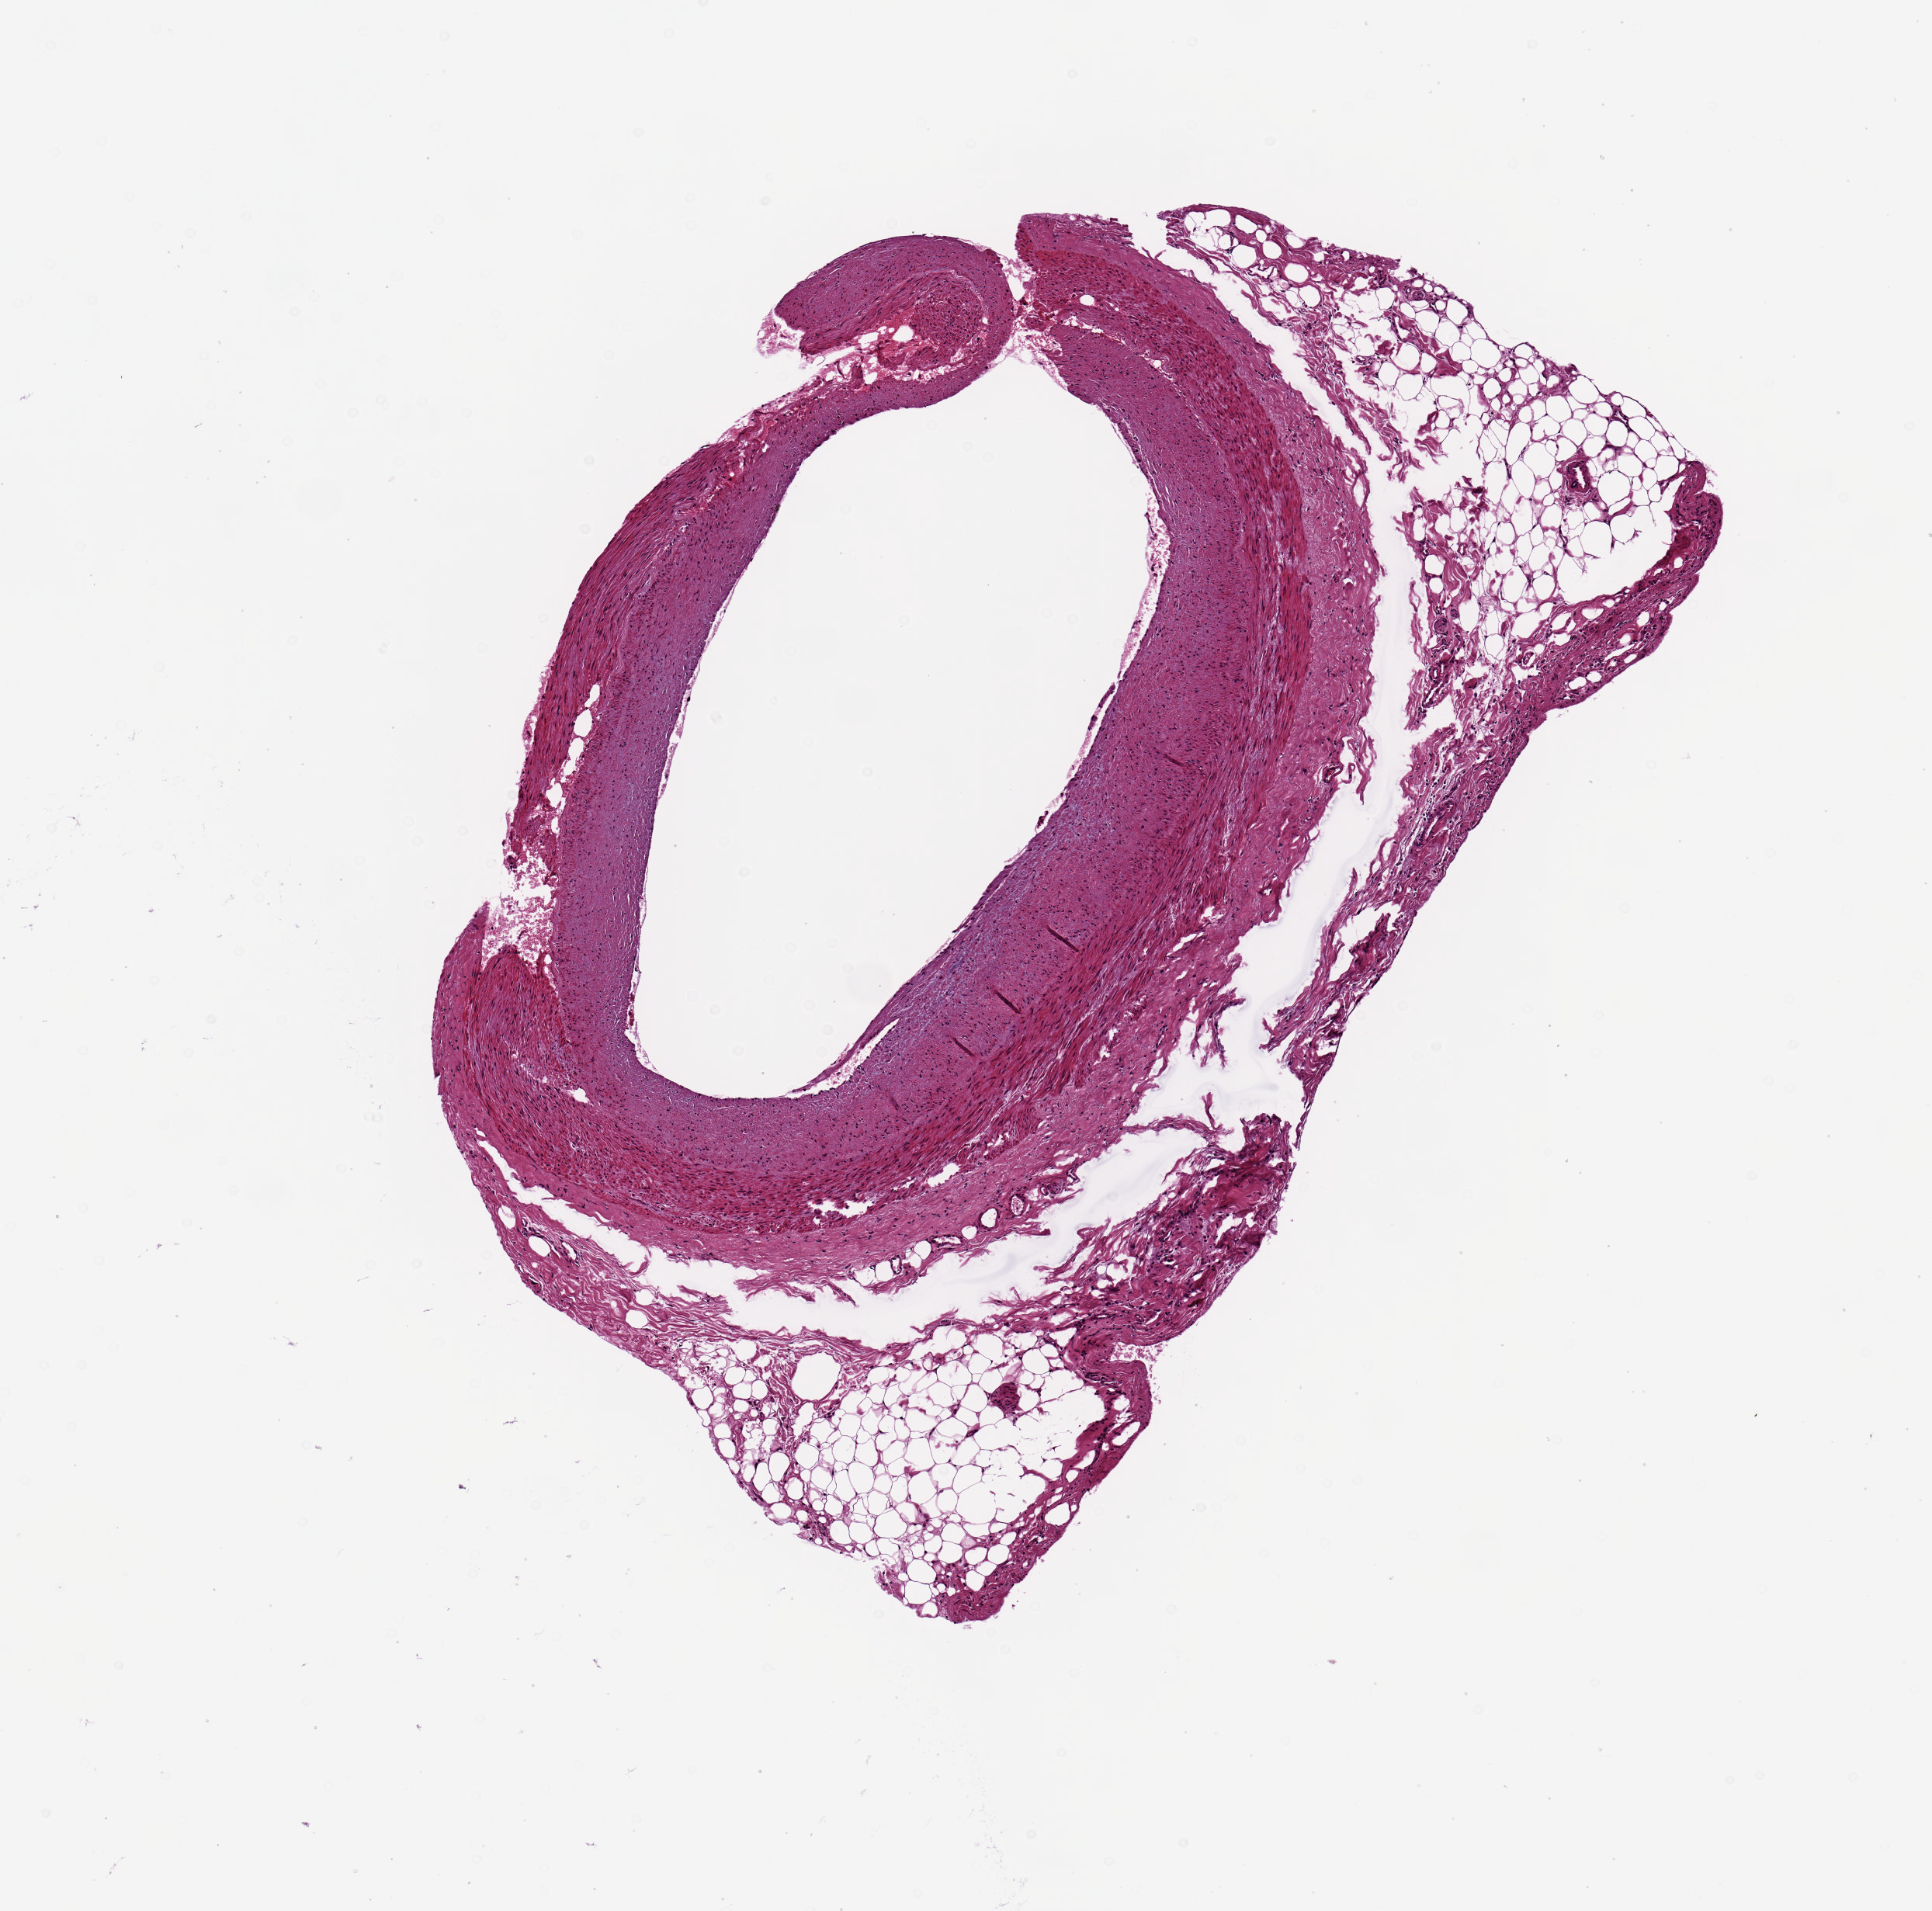
Whole-slide image, H&E stain — shown as a low-resolution overview of the whole scanned area (about 4.9 x 4.9 mm, acquisition: 20x scan). PAXgene-fixed, paraffin-embedded tissue. Sampled site (target tissue): coronary artery. Tissue donor sample. Female donor.
* pathologist's review note for this sample: 20% adipose and stroma; wide lumen